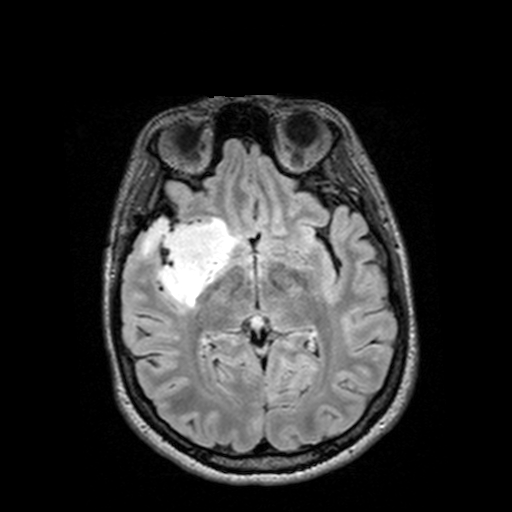
Brain MRI from a brain-tumour surgery series, one axial slice. Slice 76 of 144 in the series (ordered by position). T2 FLAIR. 1 mm slice thickness. 512 × 512 image matrix, field of view 250 × 250 mm. Case-level facts recorded for this patient, not image findings: histopathology: Astrocytoma; WHO grade: 3; IDH mutation: yes; tumour location: Right Insular Temporal.
Annotated regions visible in this slice (outlined manually by an expert reader):
- tumour: bounding box [x1, y1, x2, y2] px = [126, 219, 232, 305]